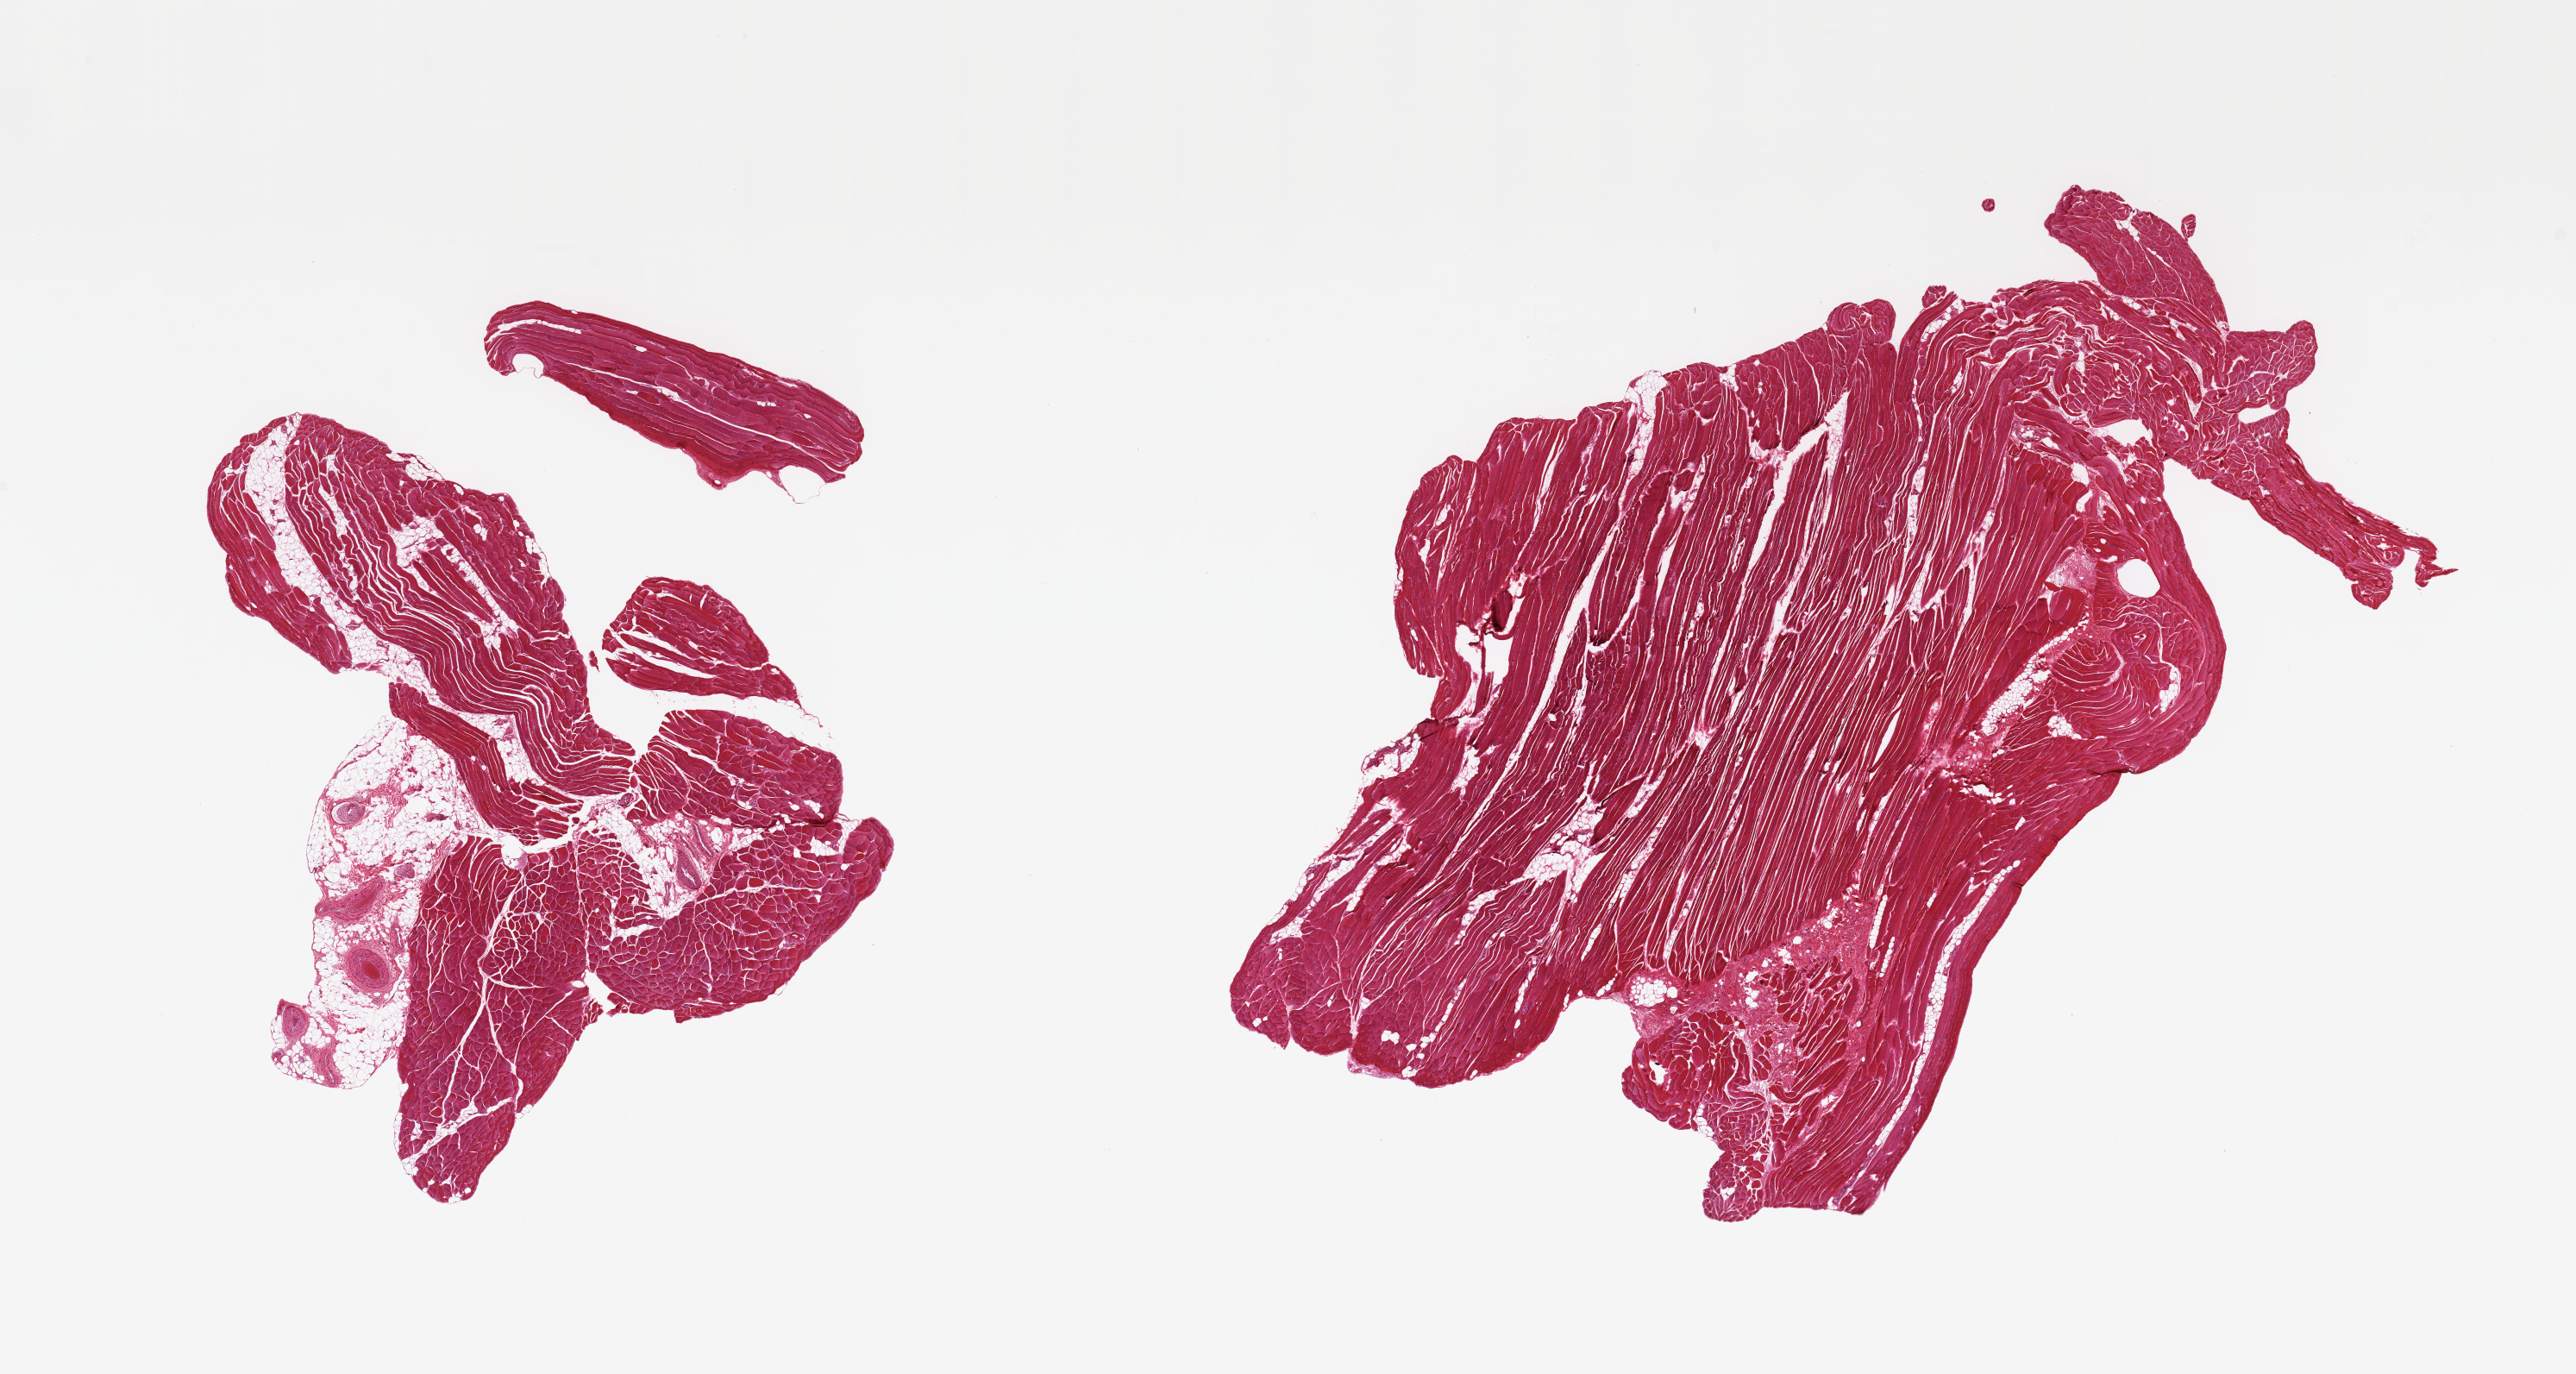
Digitized haematoxylin and eosin-stained section, brightfield, low-resolution overview of the scanned area, about 23.6 x 12.6 mm. PAXgene-fixed, paraffin-embedded tissue. Target tissue: skeletal muscle. Tissue donor sample. Donor: female.
Reviewer comment on this tissue sample: 2 pieces; 20% internal & external fat on 1 piece.